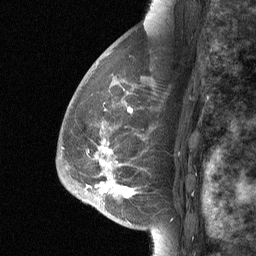
Breast MRI (dynamic contrast-enhanced), one sagittal slice; slice 43 of 64 in the series (ordered by position); dynamic contrast-enhanced study with each time point stored as its own series, time point 2 of 3 at this slice position (early post-contrast, ordered by acquisition time); 1.5 T; TE 4.8 ms, TR 27 ms; 2 mm slice thickness; 256 × 256 image matrix, field of view 180 × 180 mm. Patient: female, 56 years. Case-level facts recorded for this patient, not image findings: setting: breast cancer imaged before/during neoadjuvant chemotherapy; receptor status: HER2-positive.
Outlined on this slice (semi-automatic segmentation, software-assisted and operator-edited):
- analysis volume of interest (the breast-tissue region the enhancement analysis was run in; not a lesion): bounding box <89,83,166,214> (left, top, right, bottom; pixels)
- tumour enhancement mask (voxels above the 90 % enhancement threshold inside the analysis volume of interest): <100,110,131,197>